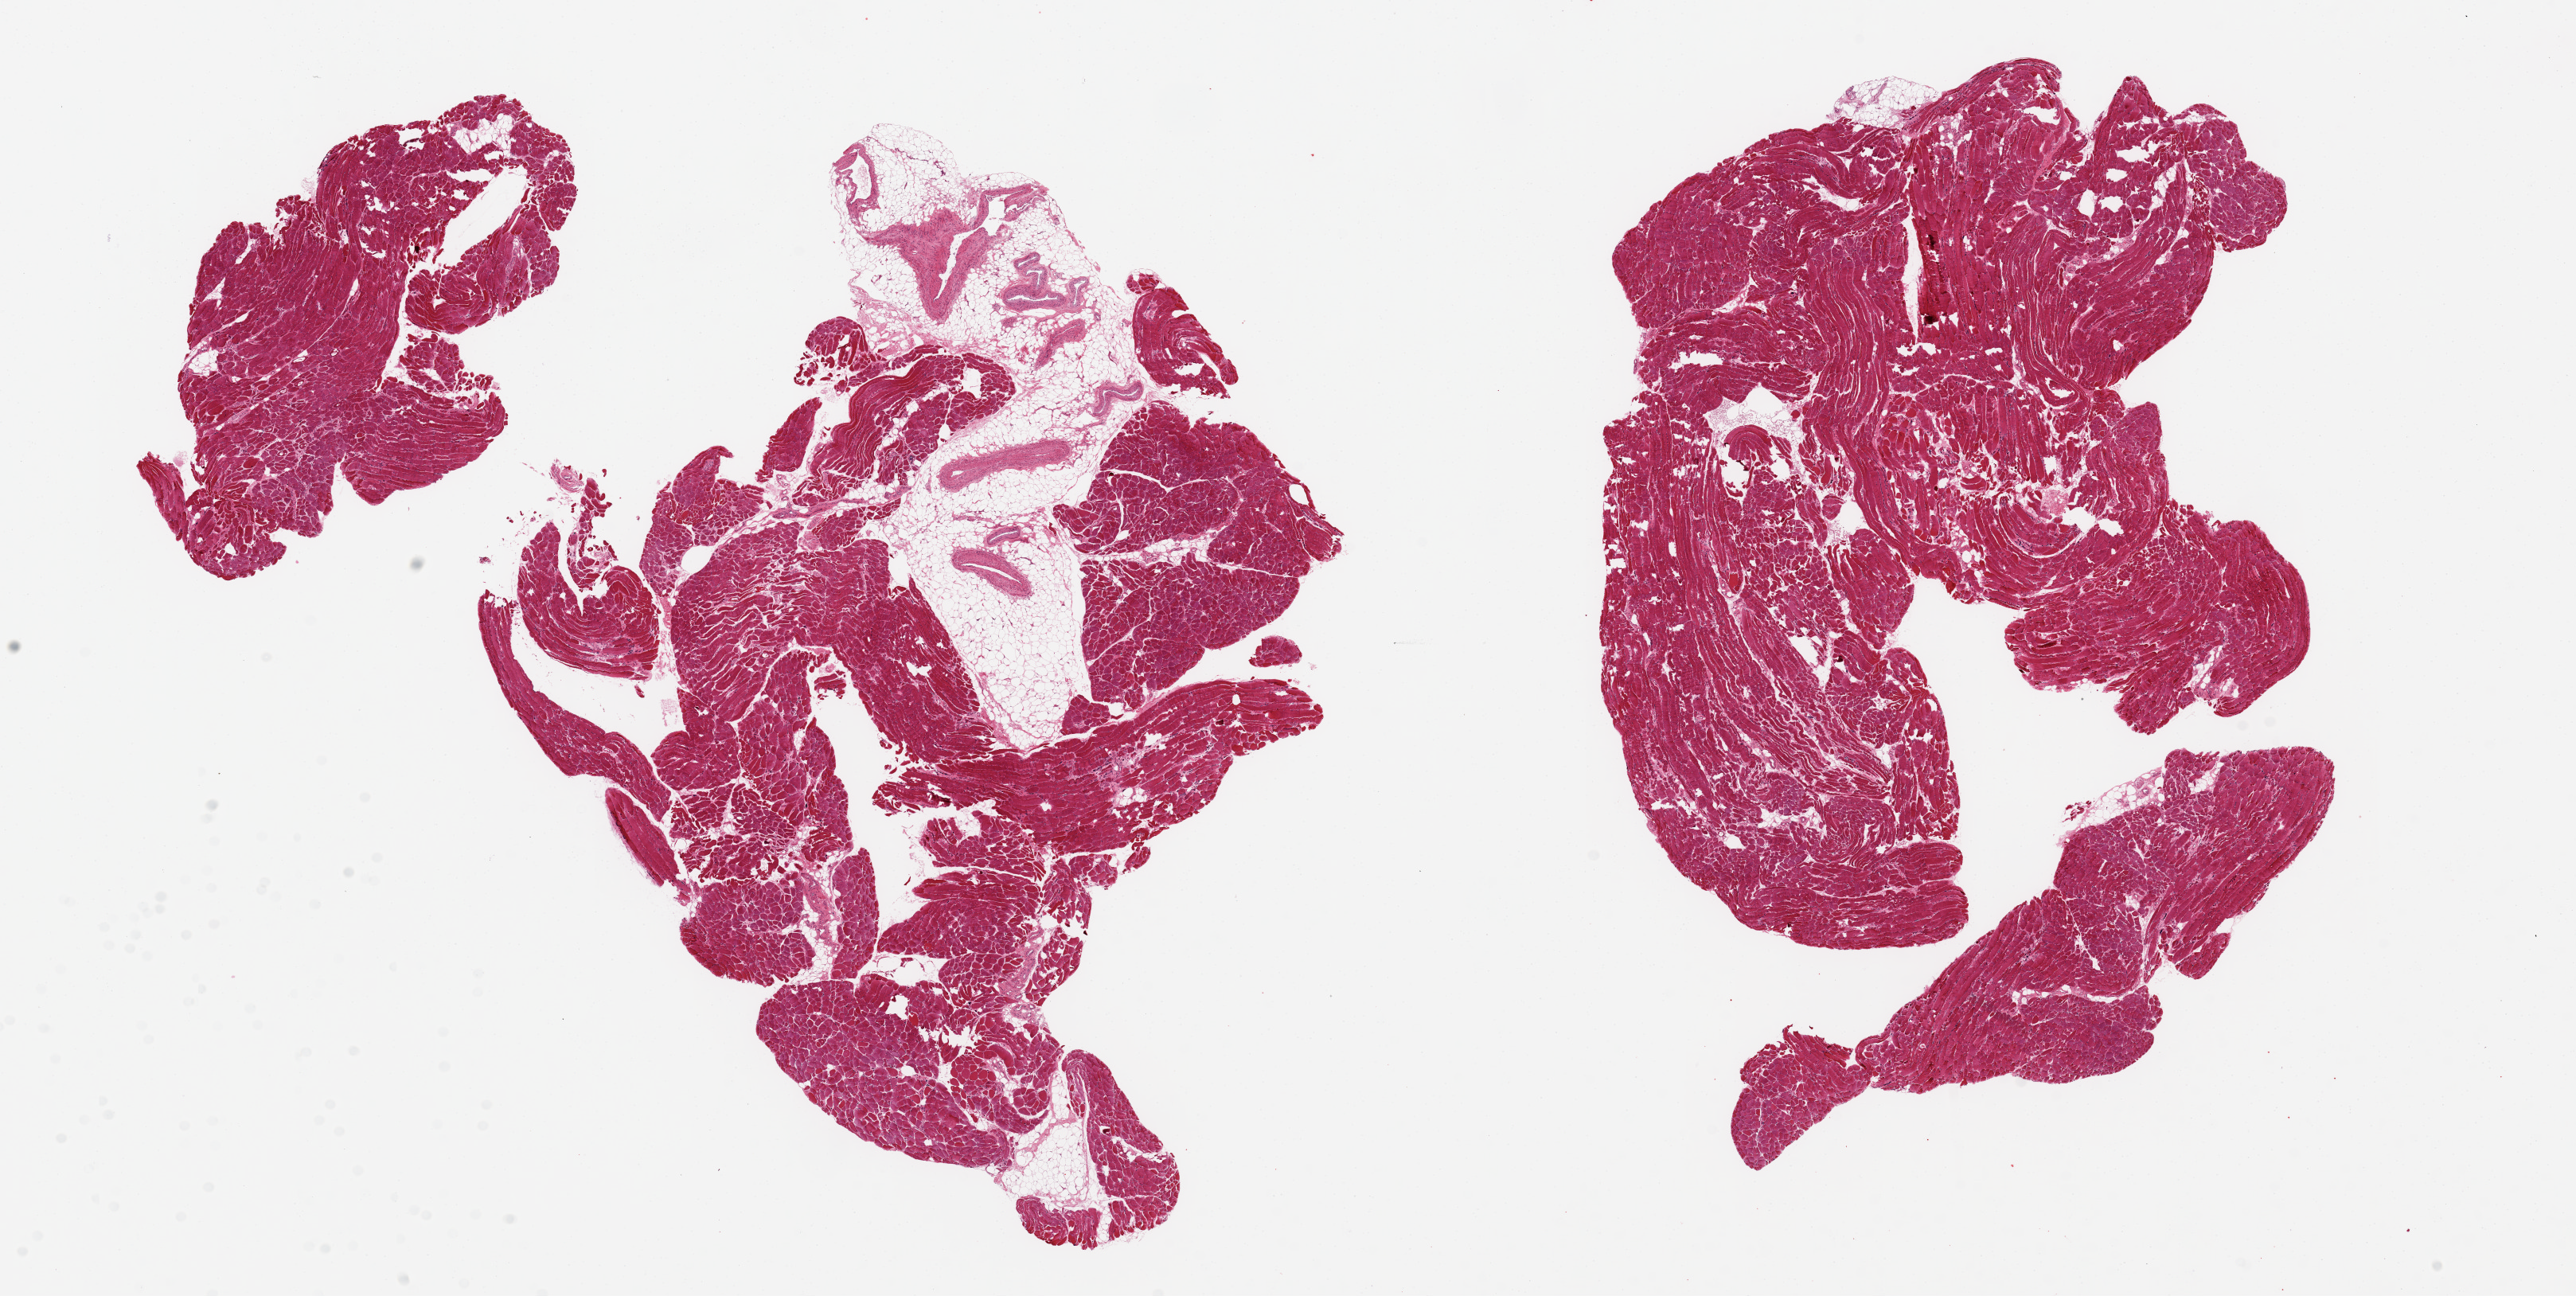
H&E whole-slide image, a low-resolution overview of the entire scanned area, about 25.6 x 12.9 mm; PAXgene-fixed, paraffin-embedded tissue; sampled site (target tissue): skeletal muscle; donor tissue sample. Donor: female.
Pathologist's review note for this sample: 2 ~ 8x8mm aliquots, fragmented, one with 5x1.5mm central fatty area.